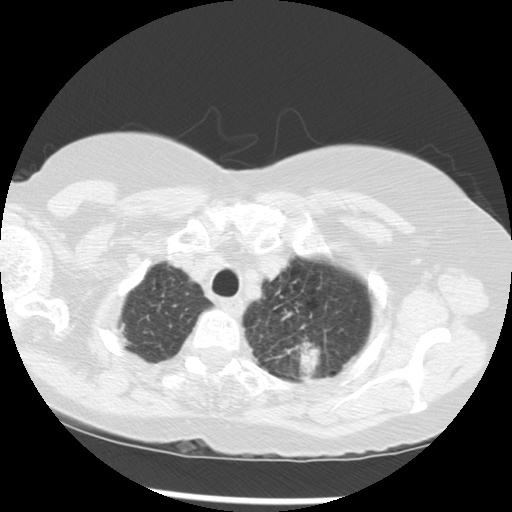
Chest CT (low-dose screening protocol), one axial image, third annual screen, lung window (W 1500 / L -600 HU), 2.5 mm slice thickness, slice 246 of 283 in the series, 512 × 512 image matrix. Female, age 70 years at enrolment. Current smoker at enrolment.
Lesion marked by an expert reader, bounding box <244,294,343,381> (left, top, right, bottom; pixels). Reader record for this screening exam (exam-level; its link to the box is not recorded): non-calcified nodule or mass ≥4 mm, left upper lobe, 32 × 26 mm, spiculated (stellate) margins, soft tissue attenuation, pre-existing on the prior screen: yes; interval growth: yes. Participant outcome: lung cancer diagnosed 24 days after this screen — neoplasm, malignant, left upper lobe, stage IIIB (AJCC 6th edition), 40 mm at pathology.